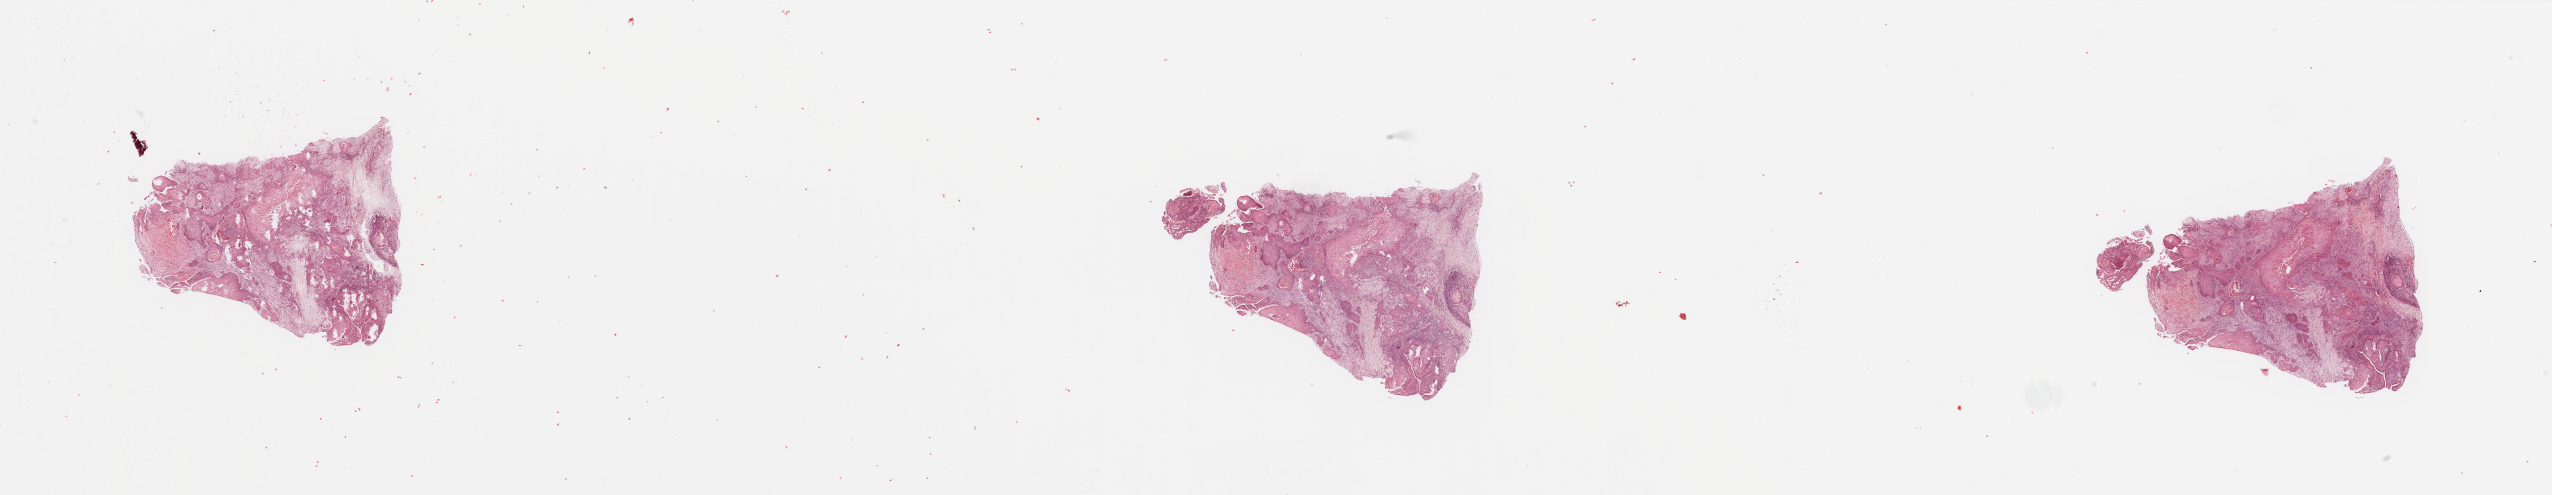
H&E-stained whole-slide image, low-resolution overview of the scanned area, about 40.4 x 7.8 mm (from a 20x scan). Tumour tissue sample, sampled site: tongue. 59-year-old male patient. Composition of this section per pathologist review: tumour nuclei 80%, necrosis 5%.
Diagnosis: Squamous cell carcinoma, NOS (tongue, NOS).